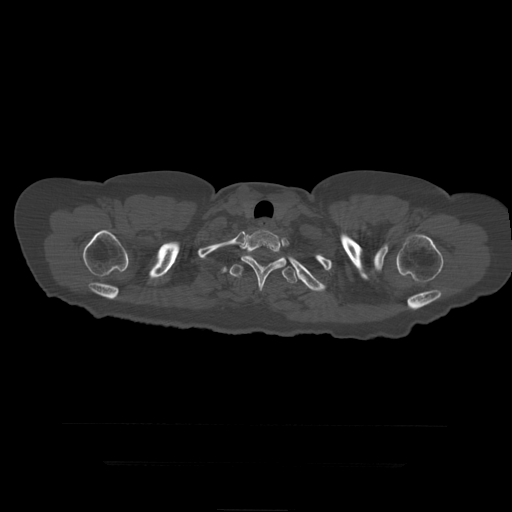
CT including the spine, one axial slice; position 372 of 399 along the scan axis; bone window (W 1800 / L 400 HU); 1.25 mm slice thickness; 512 × 512 image matrix. Patient age 41 years. From the clinical record (not read from this slice): primary cancer: breast.
Outlined on this slice (semi-automatic segmentation, software-assisted and operator-edited):
- T2 vertebra: bounding box <241,230,287,292> (left, top, right, bottom; pixels)
- T3 vertebra: <229,254,298,284>